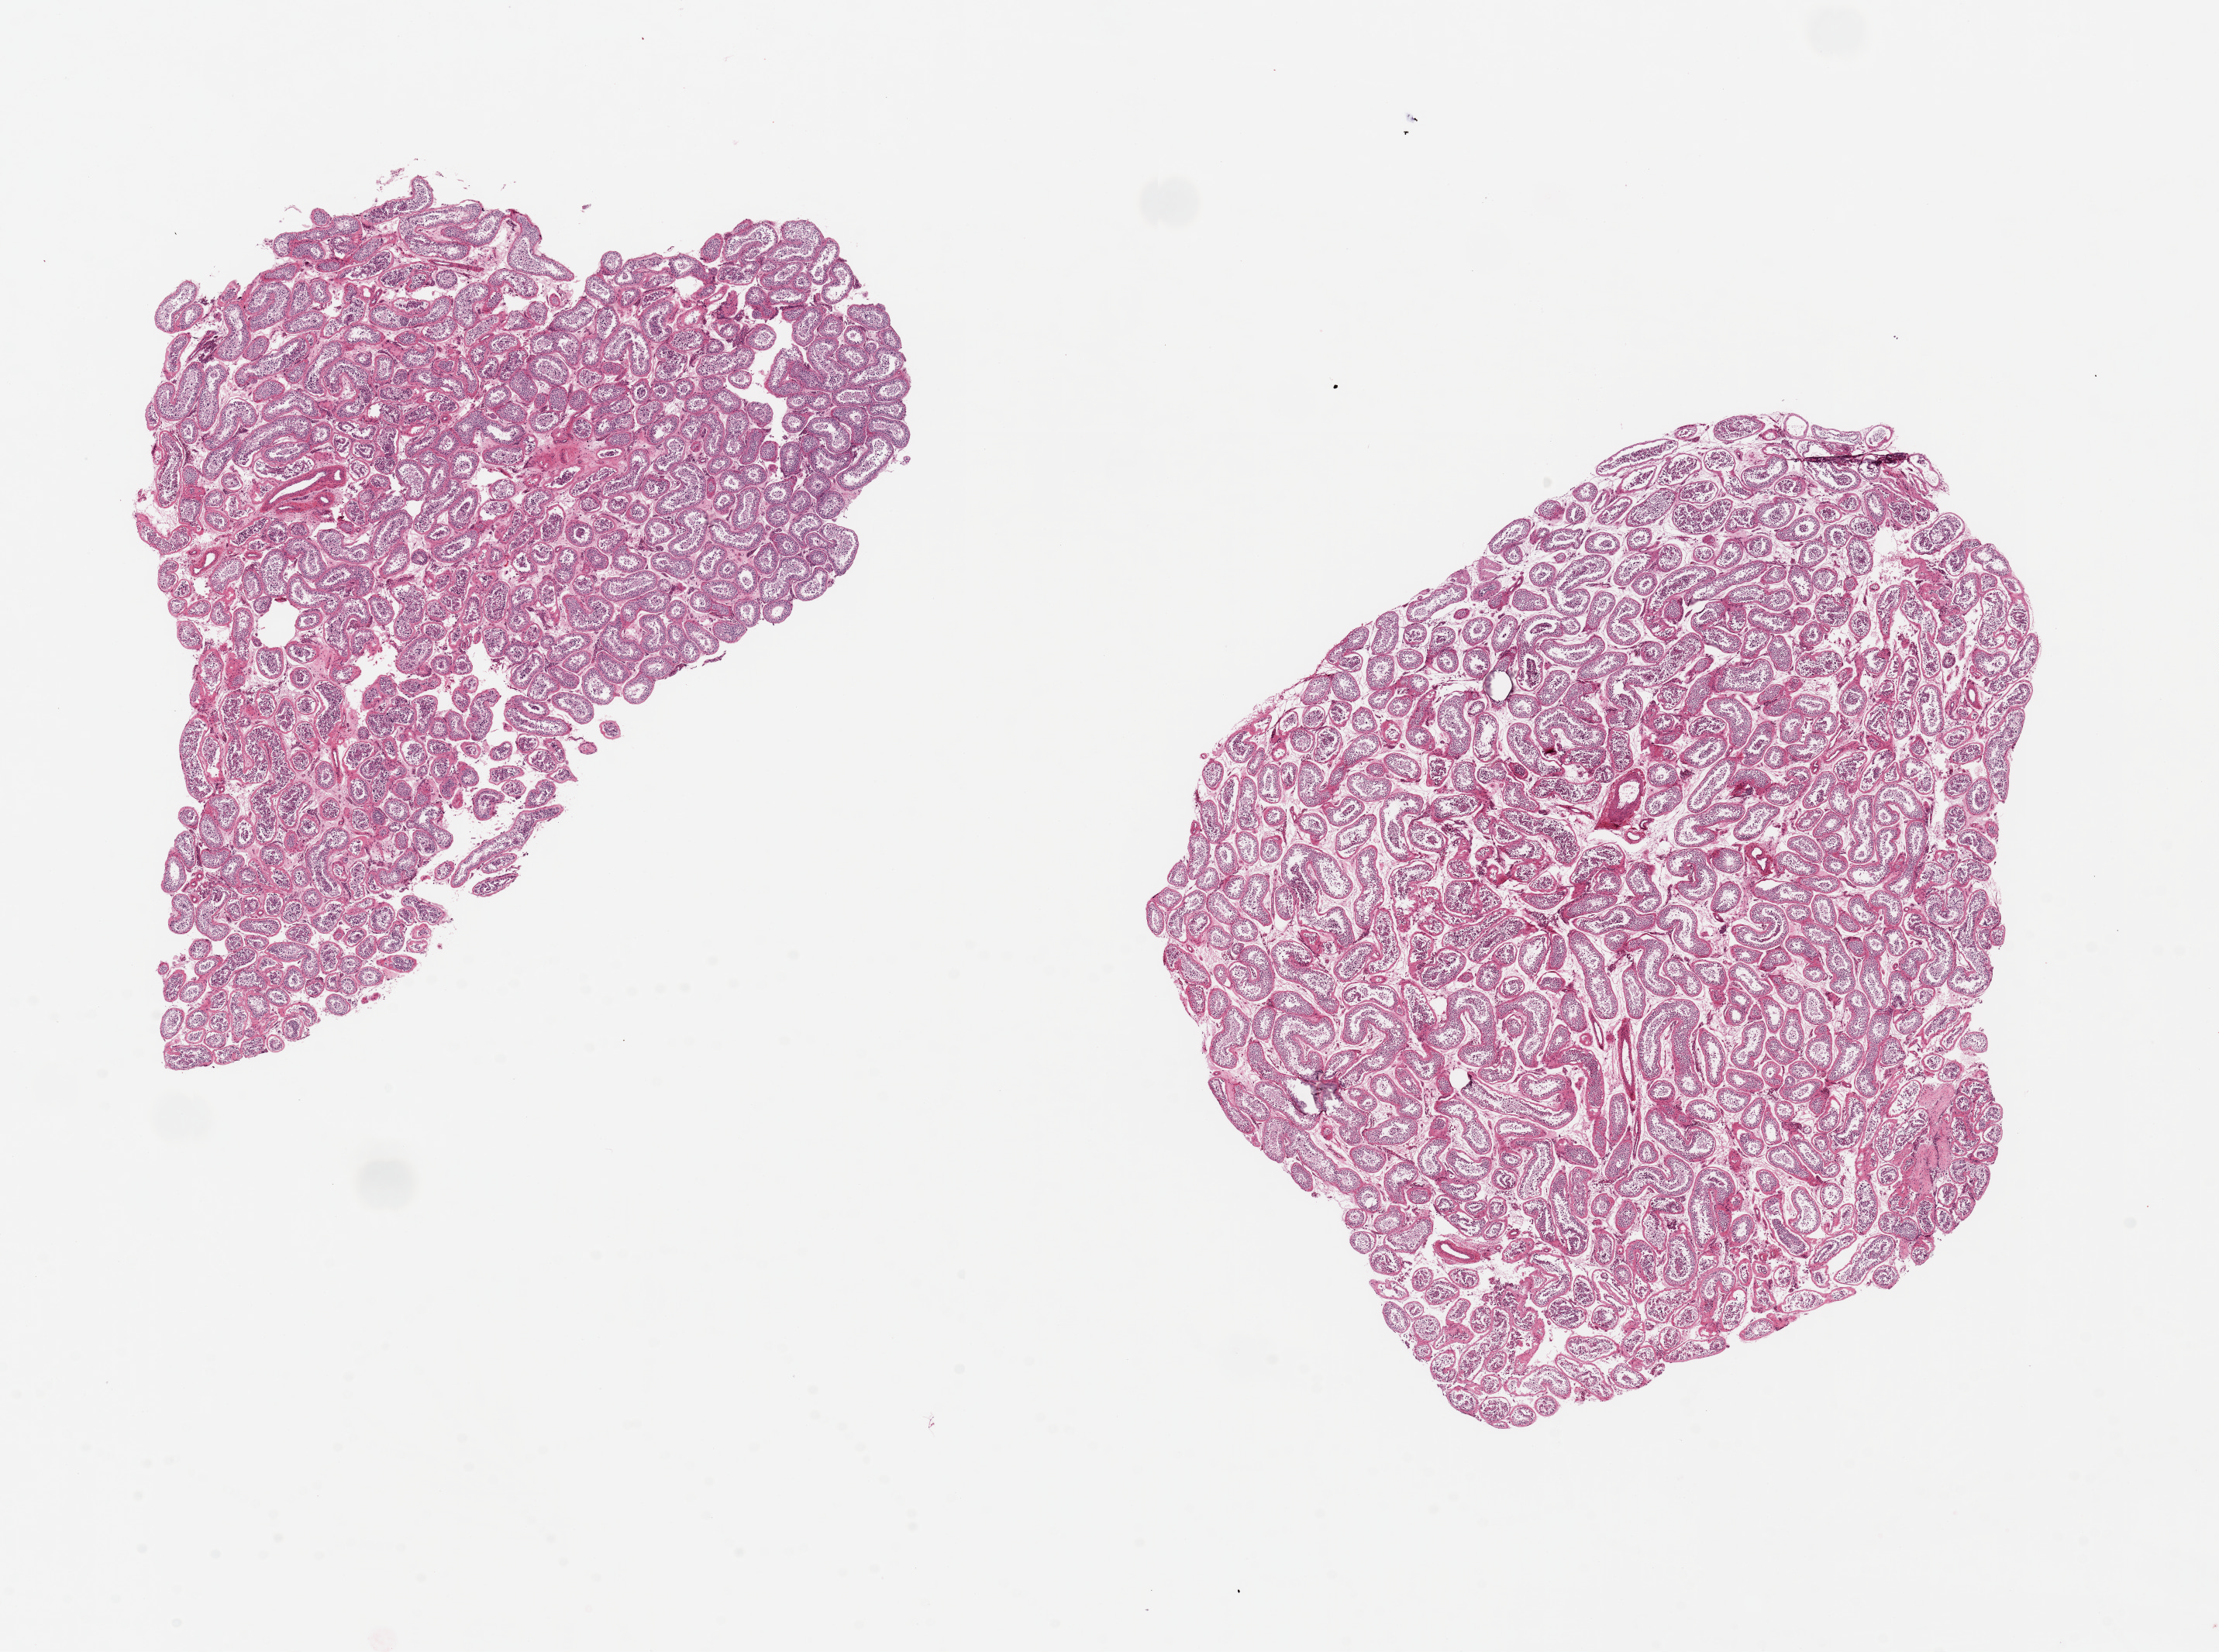
Digitized hematoxylin and eosin (H&E)-stained section — shown as a low-resolution overview of the whole scanned area (about 22.6 x 16.9 mm); PAXgene-fixed, paraffin-embedded tissue; sampled site (target tissue): testis; tissue donor sample.
• reviewer comment on this tissue sample: 2 pieces ~10x7mm, spermatogenesis present